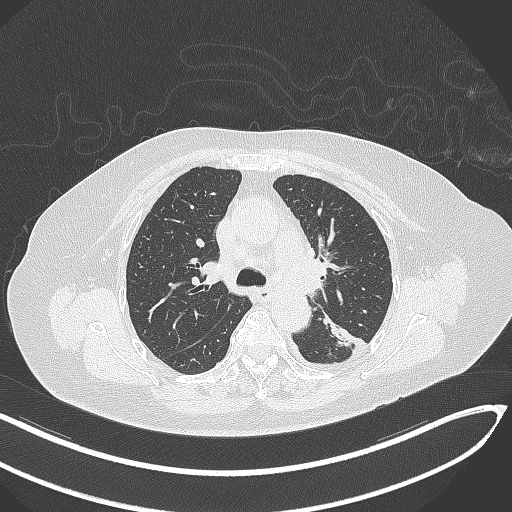
Chest CT, one axial slice; position 210 of 270 along the scan axis; reconstruction kernel B70f; 120 kVp; lung window (W 1500 / L -600 HU); 512 × 512 image matrix. Patient: female, 76 years. Case-level facts recorded for this patient, not image findings: clinical TNM (as recorded): T1c N0 M0.
Annotated regions visible in this slice (rectangle marked by the reading radiologist):
- lung tumour (recorded histology: adenocarcinoma): bounding box [x1, y1, x2, y2] px = [318, 314, 355, 354]